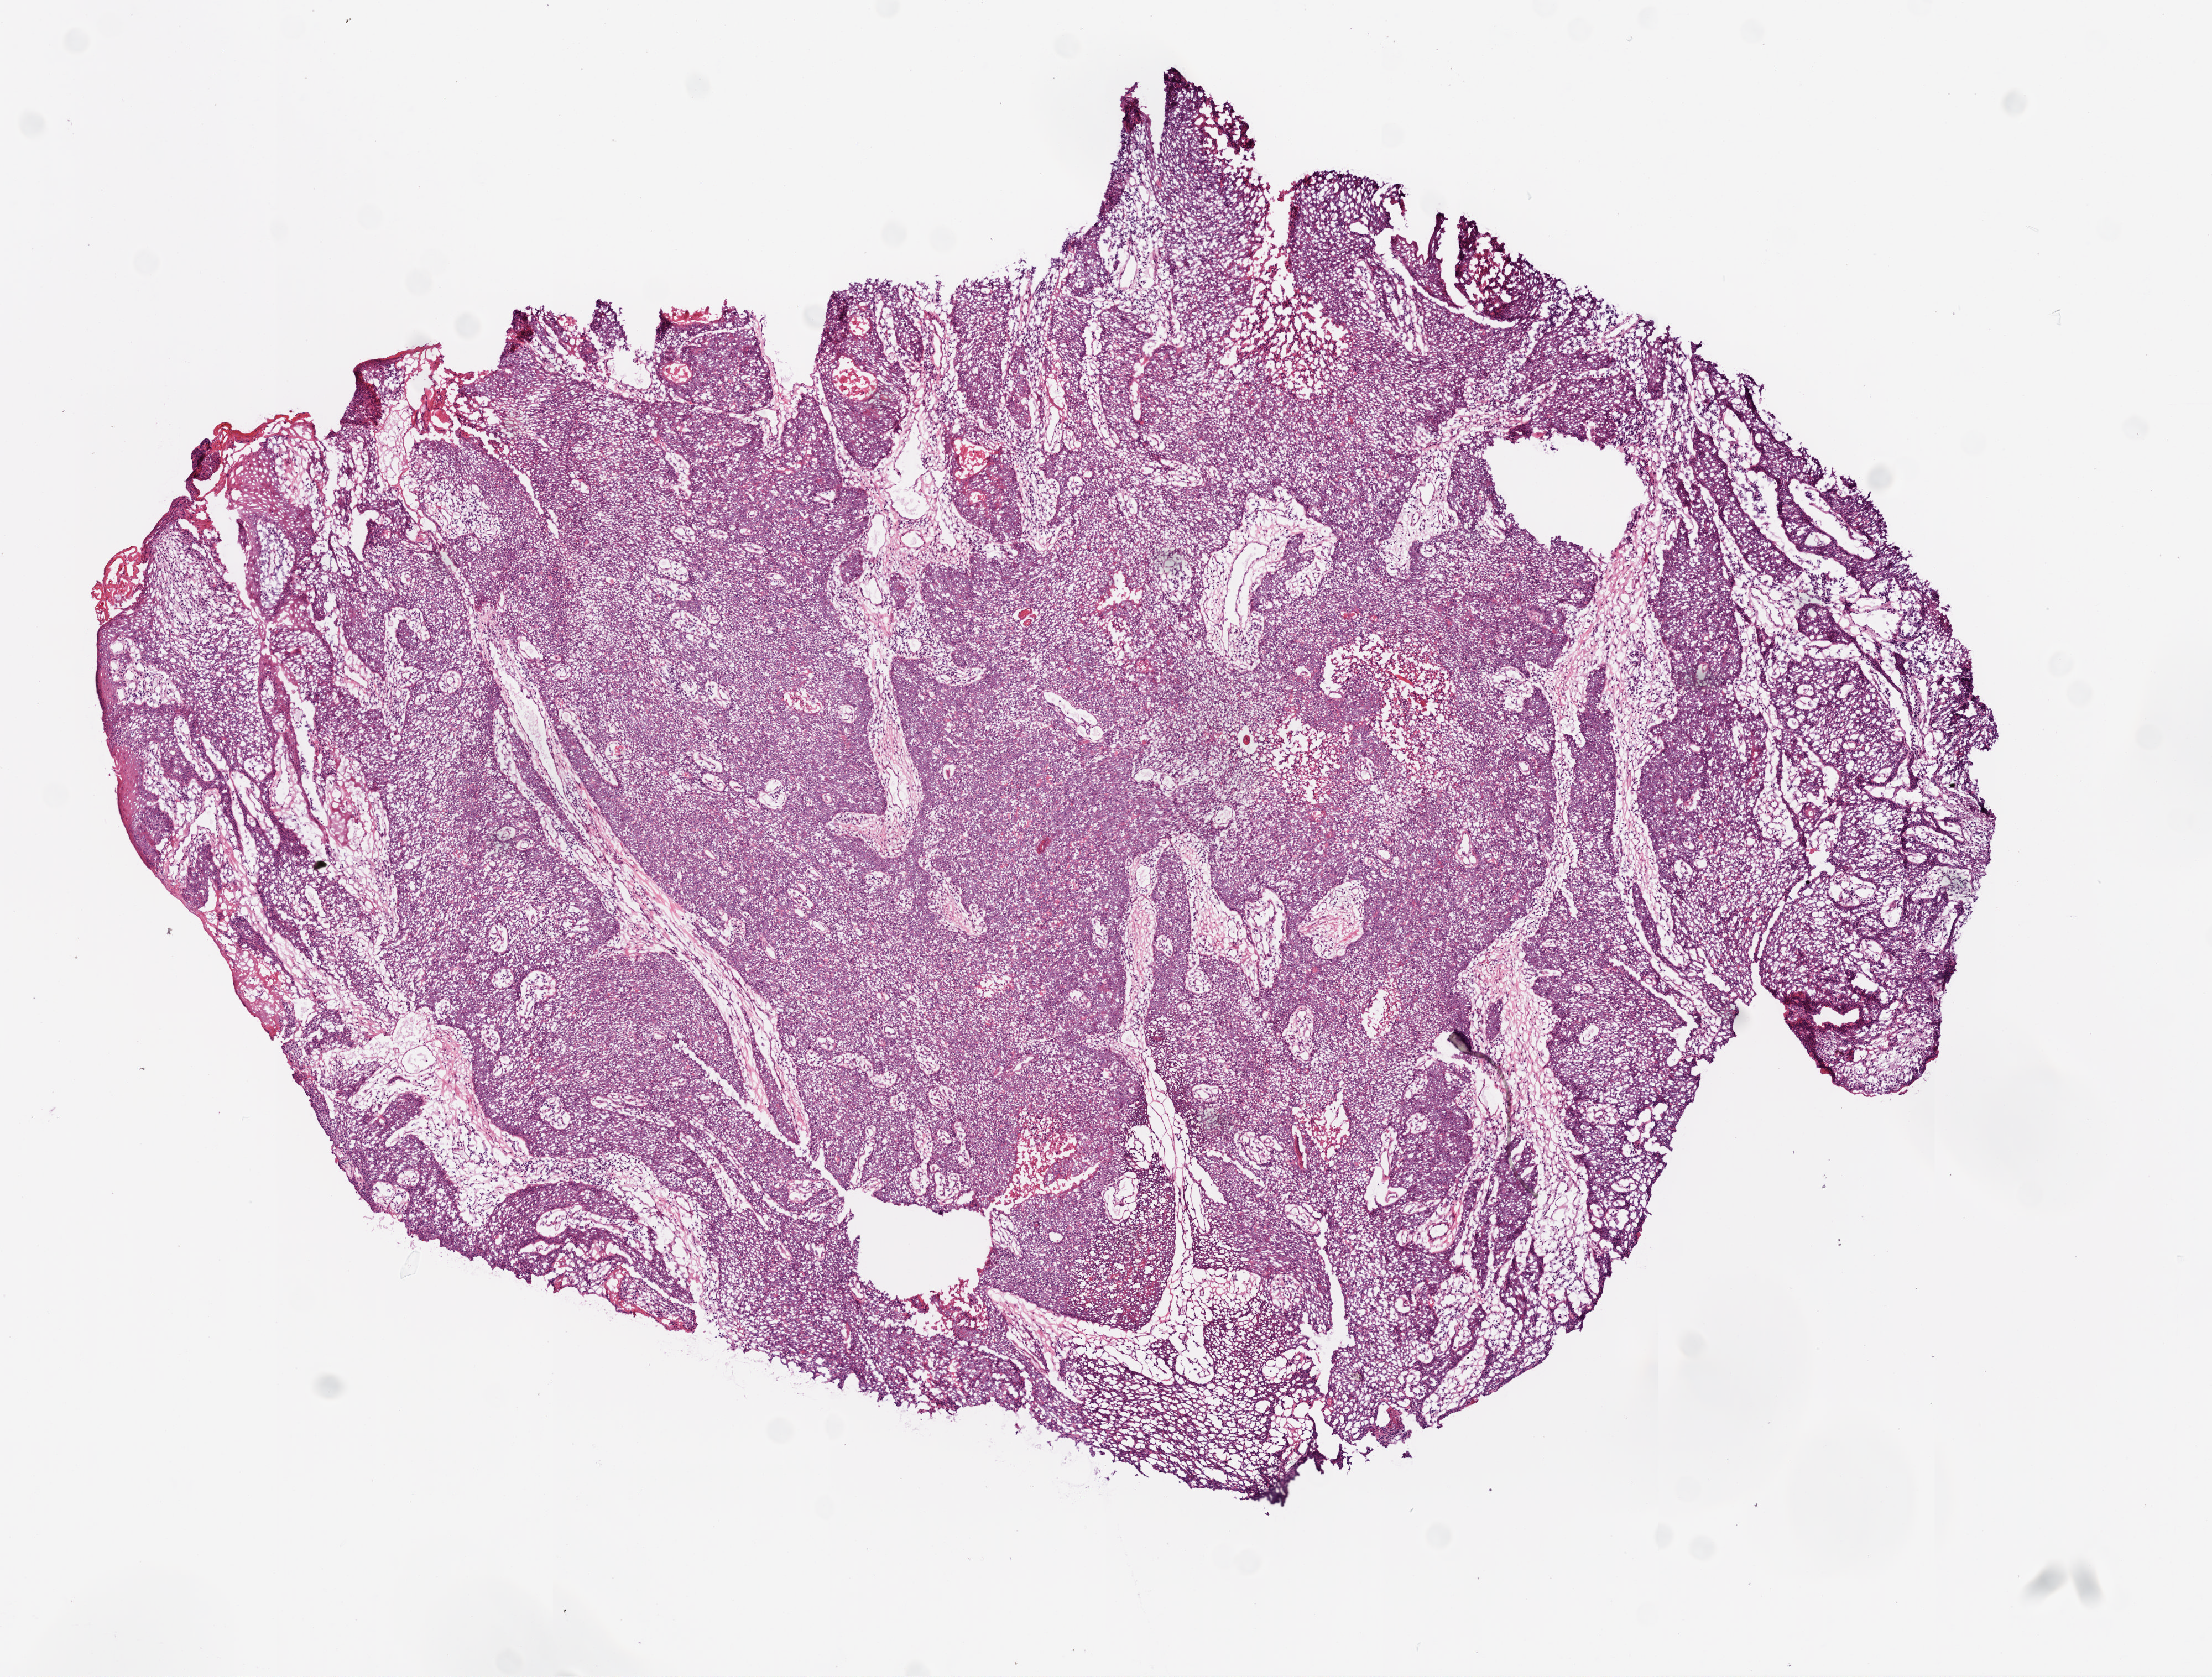
Digitized H&E-stained tissue section (whole slide) — a low-resolution overview of the entire scanned area, about 8.0 x 6.1 mm (from a 20x scan), frozen section from the bottom of the tissue portion, primary tumour sample from the head and neck. Male, age 51 years at initial diagnosis. Histologic grade: G2 (moderately differentiated). Composition of this section per pathologist review: tumour cells 82%, tumour nuclei 80%, normal cells 0%, stromal cells 15%, necrosis 3%.
• histologic diagnosis: Squamous cell carcinoma, NOS (tonsil, NOS)